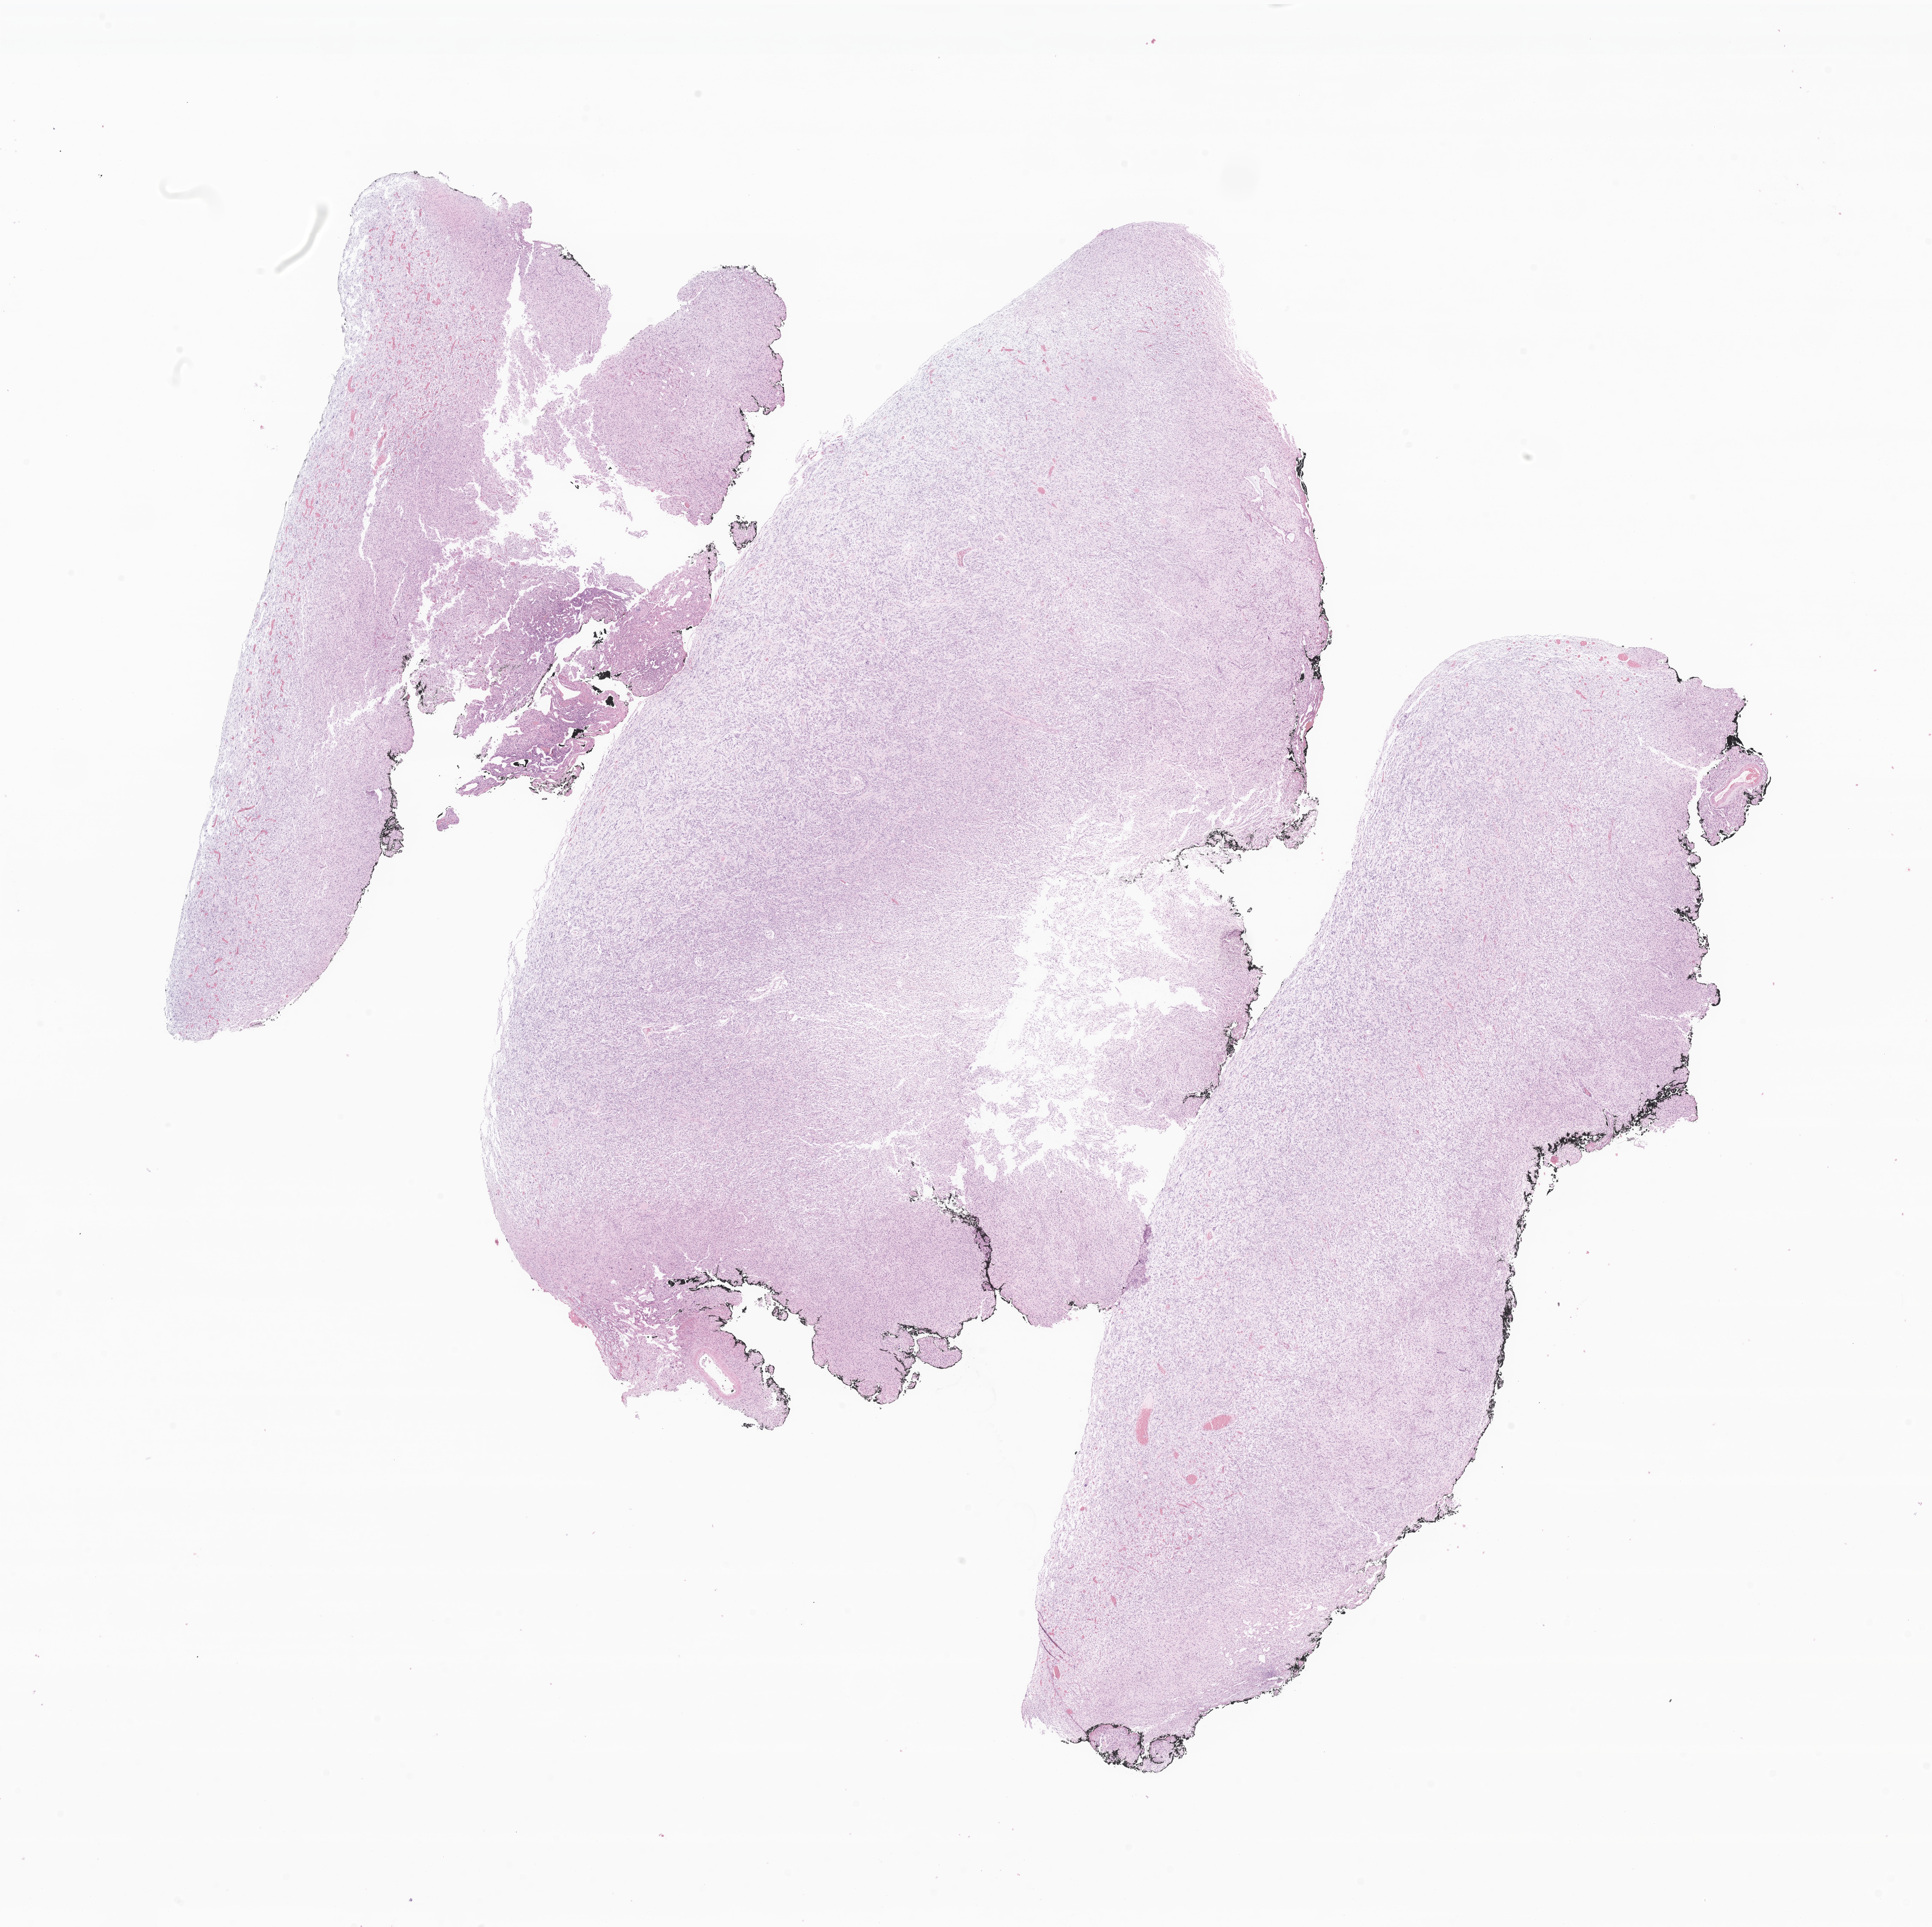
H&E whole-slide image of tumor tissue from the temporal lobe, whole scanned area (about 23.1 x 23.0 mm) shown as a low-resolution overview, formalin-fixed, paraffin-embedded (FFPE) tissue. Patient female; age 147 months (12 years 3 months).
Diagnosis (ICD-O-3 morphology term): Pleomorphic xanthoastrocytoma, NOS.